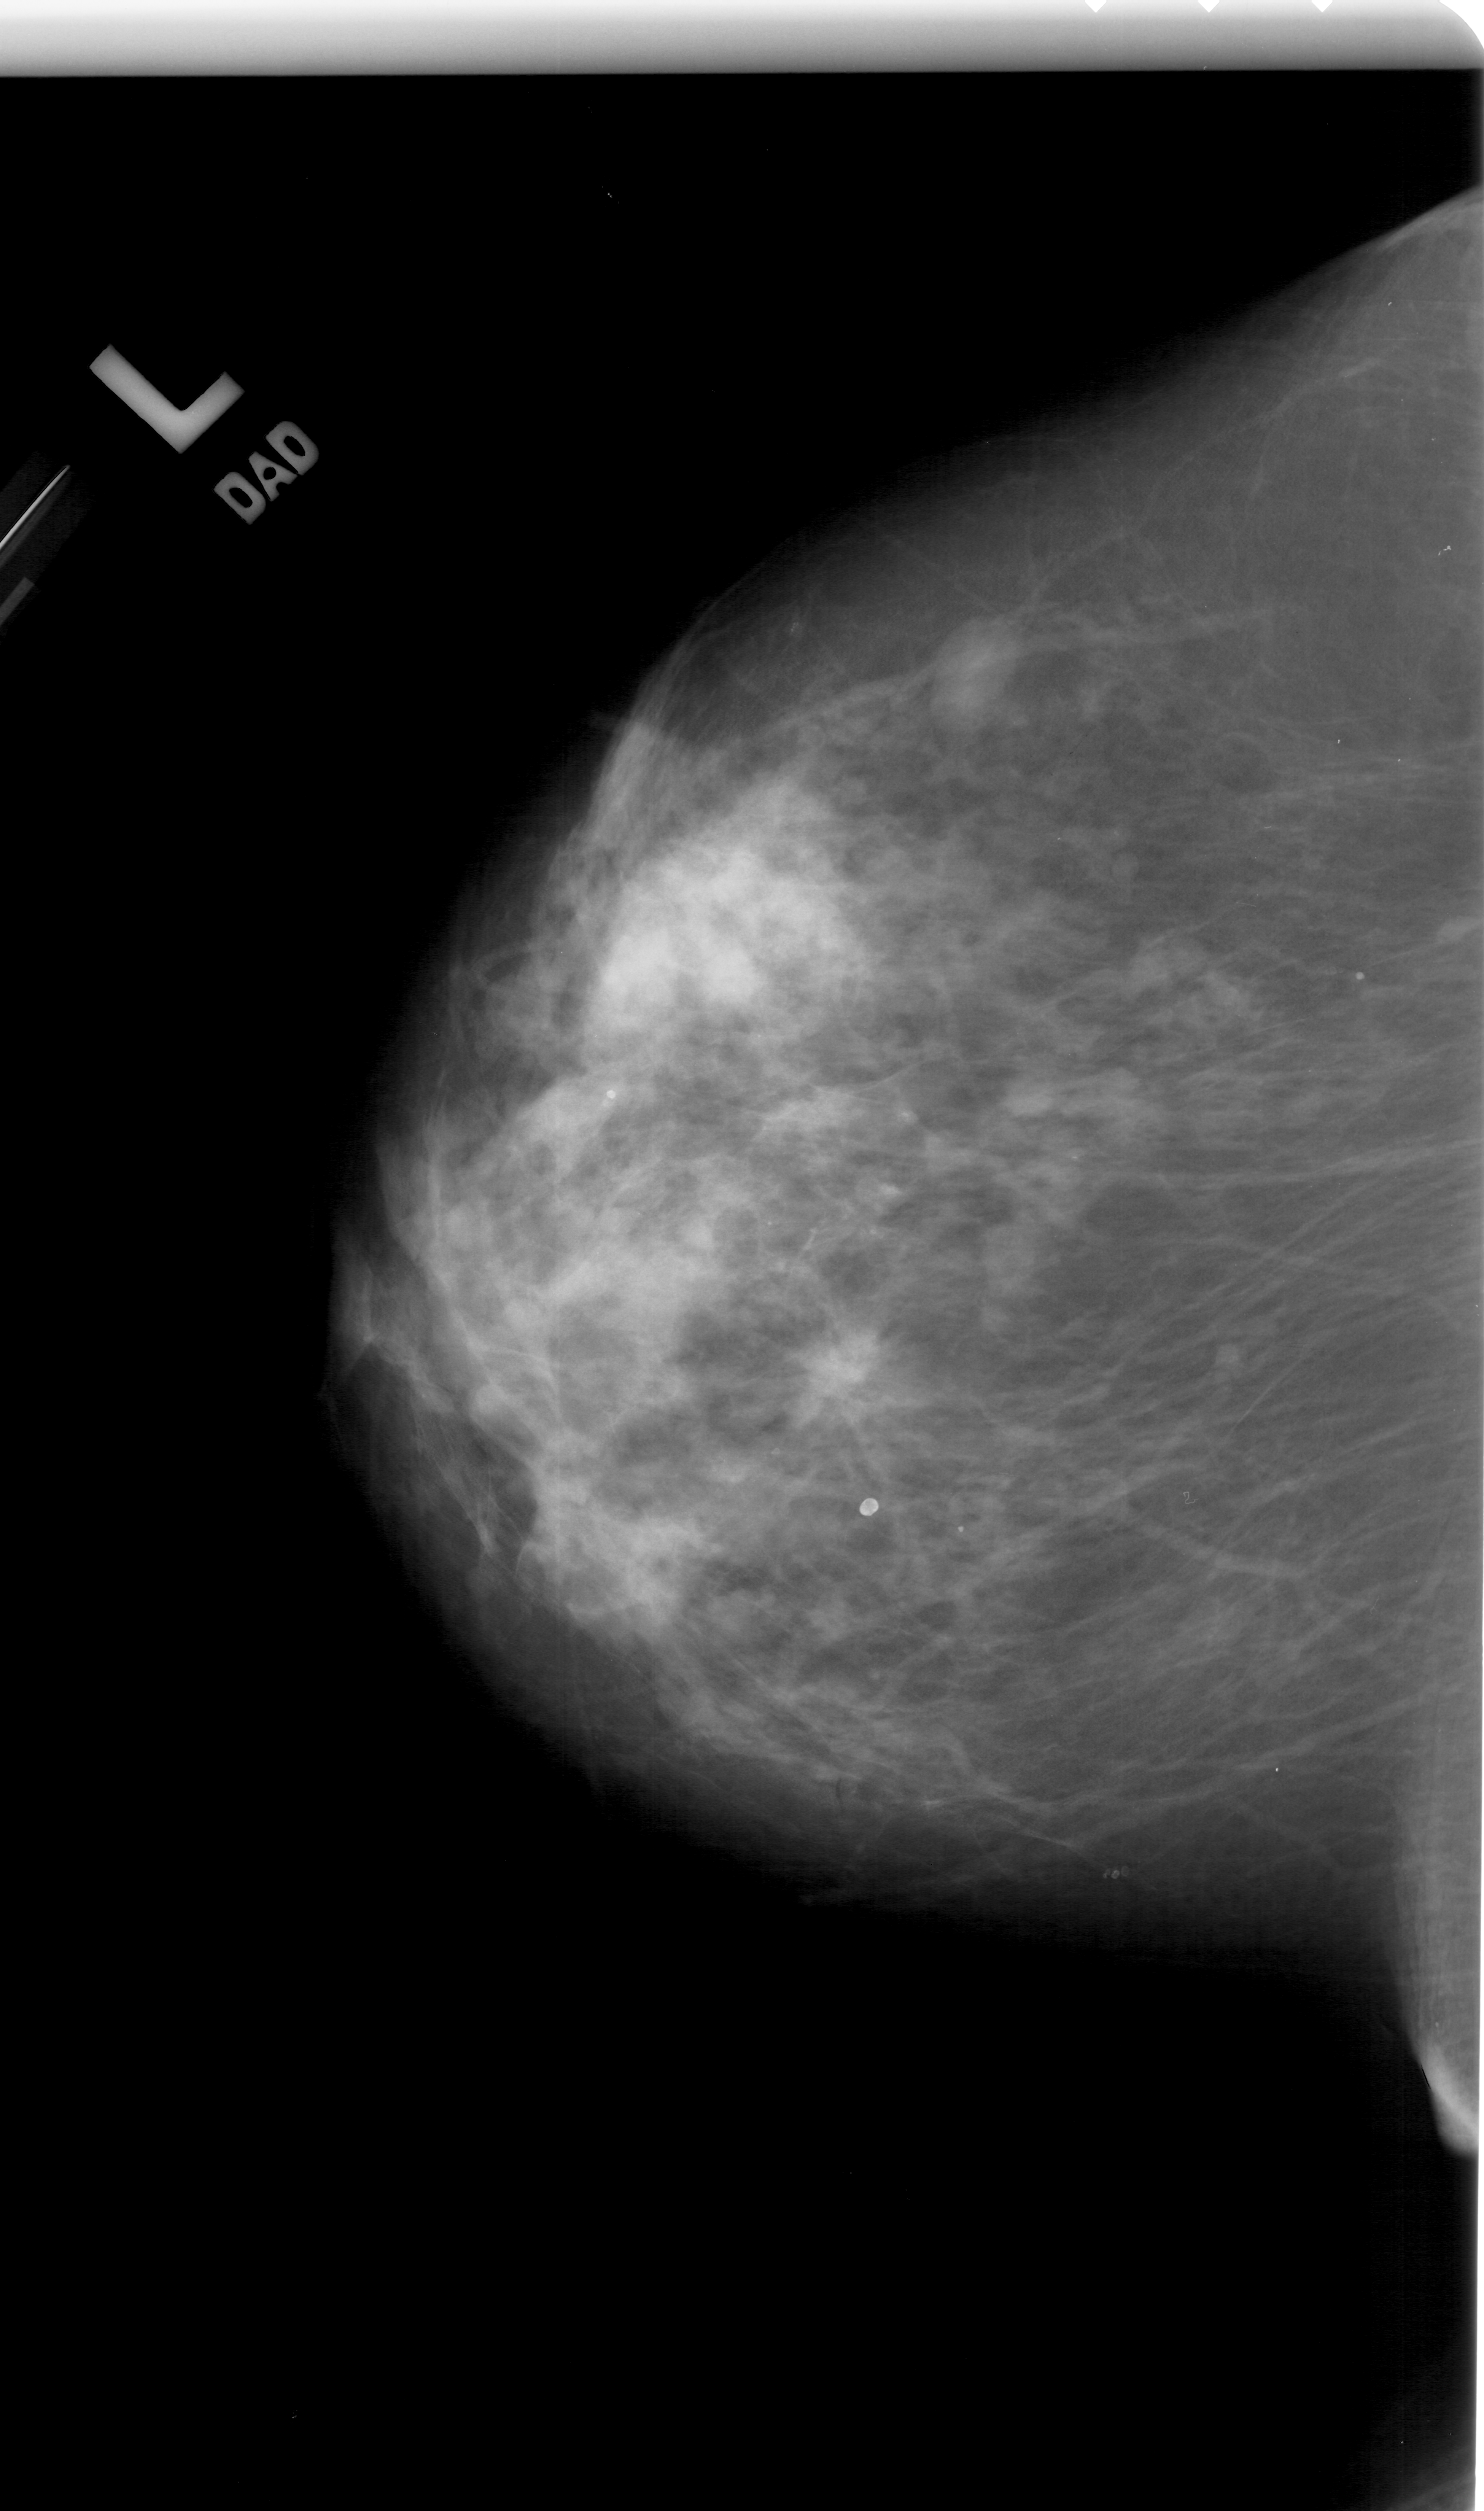
Scanned film-screen mammogram; left breast; CC view; BI-RADS breast density category 3 (scale 1–4); 1484 × 2511 image matrix.
Marked abnormalities (boxes around the expert regions of interest):
- mass, shape architectural distortion, margins spiculated; BI-RADS assessment category 5; pathology (as recorded): malignant: bounding box <783,1299,917,1413> (left, top, right, bottom; pixels)